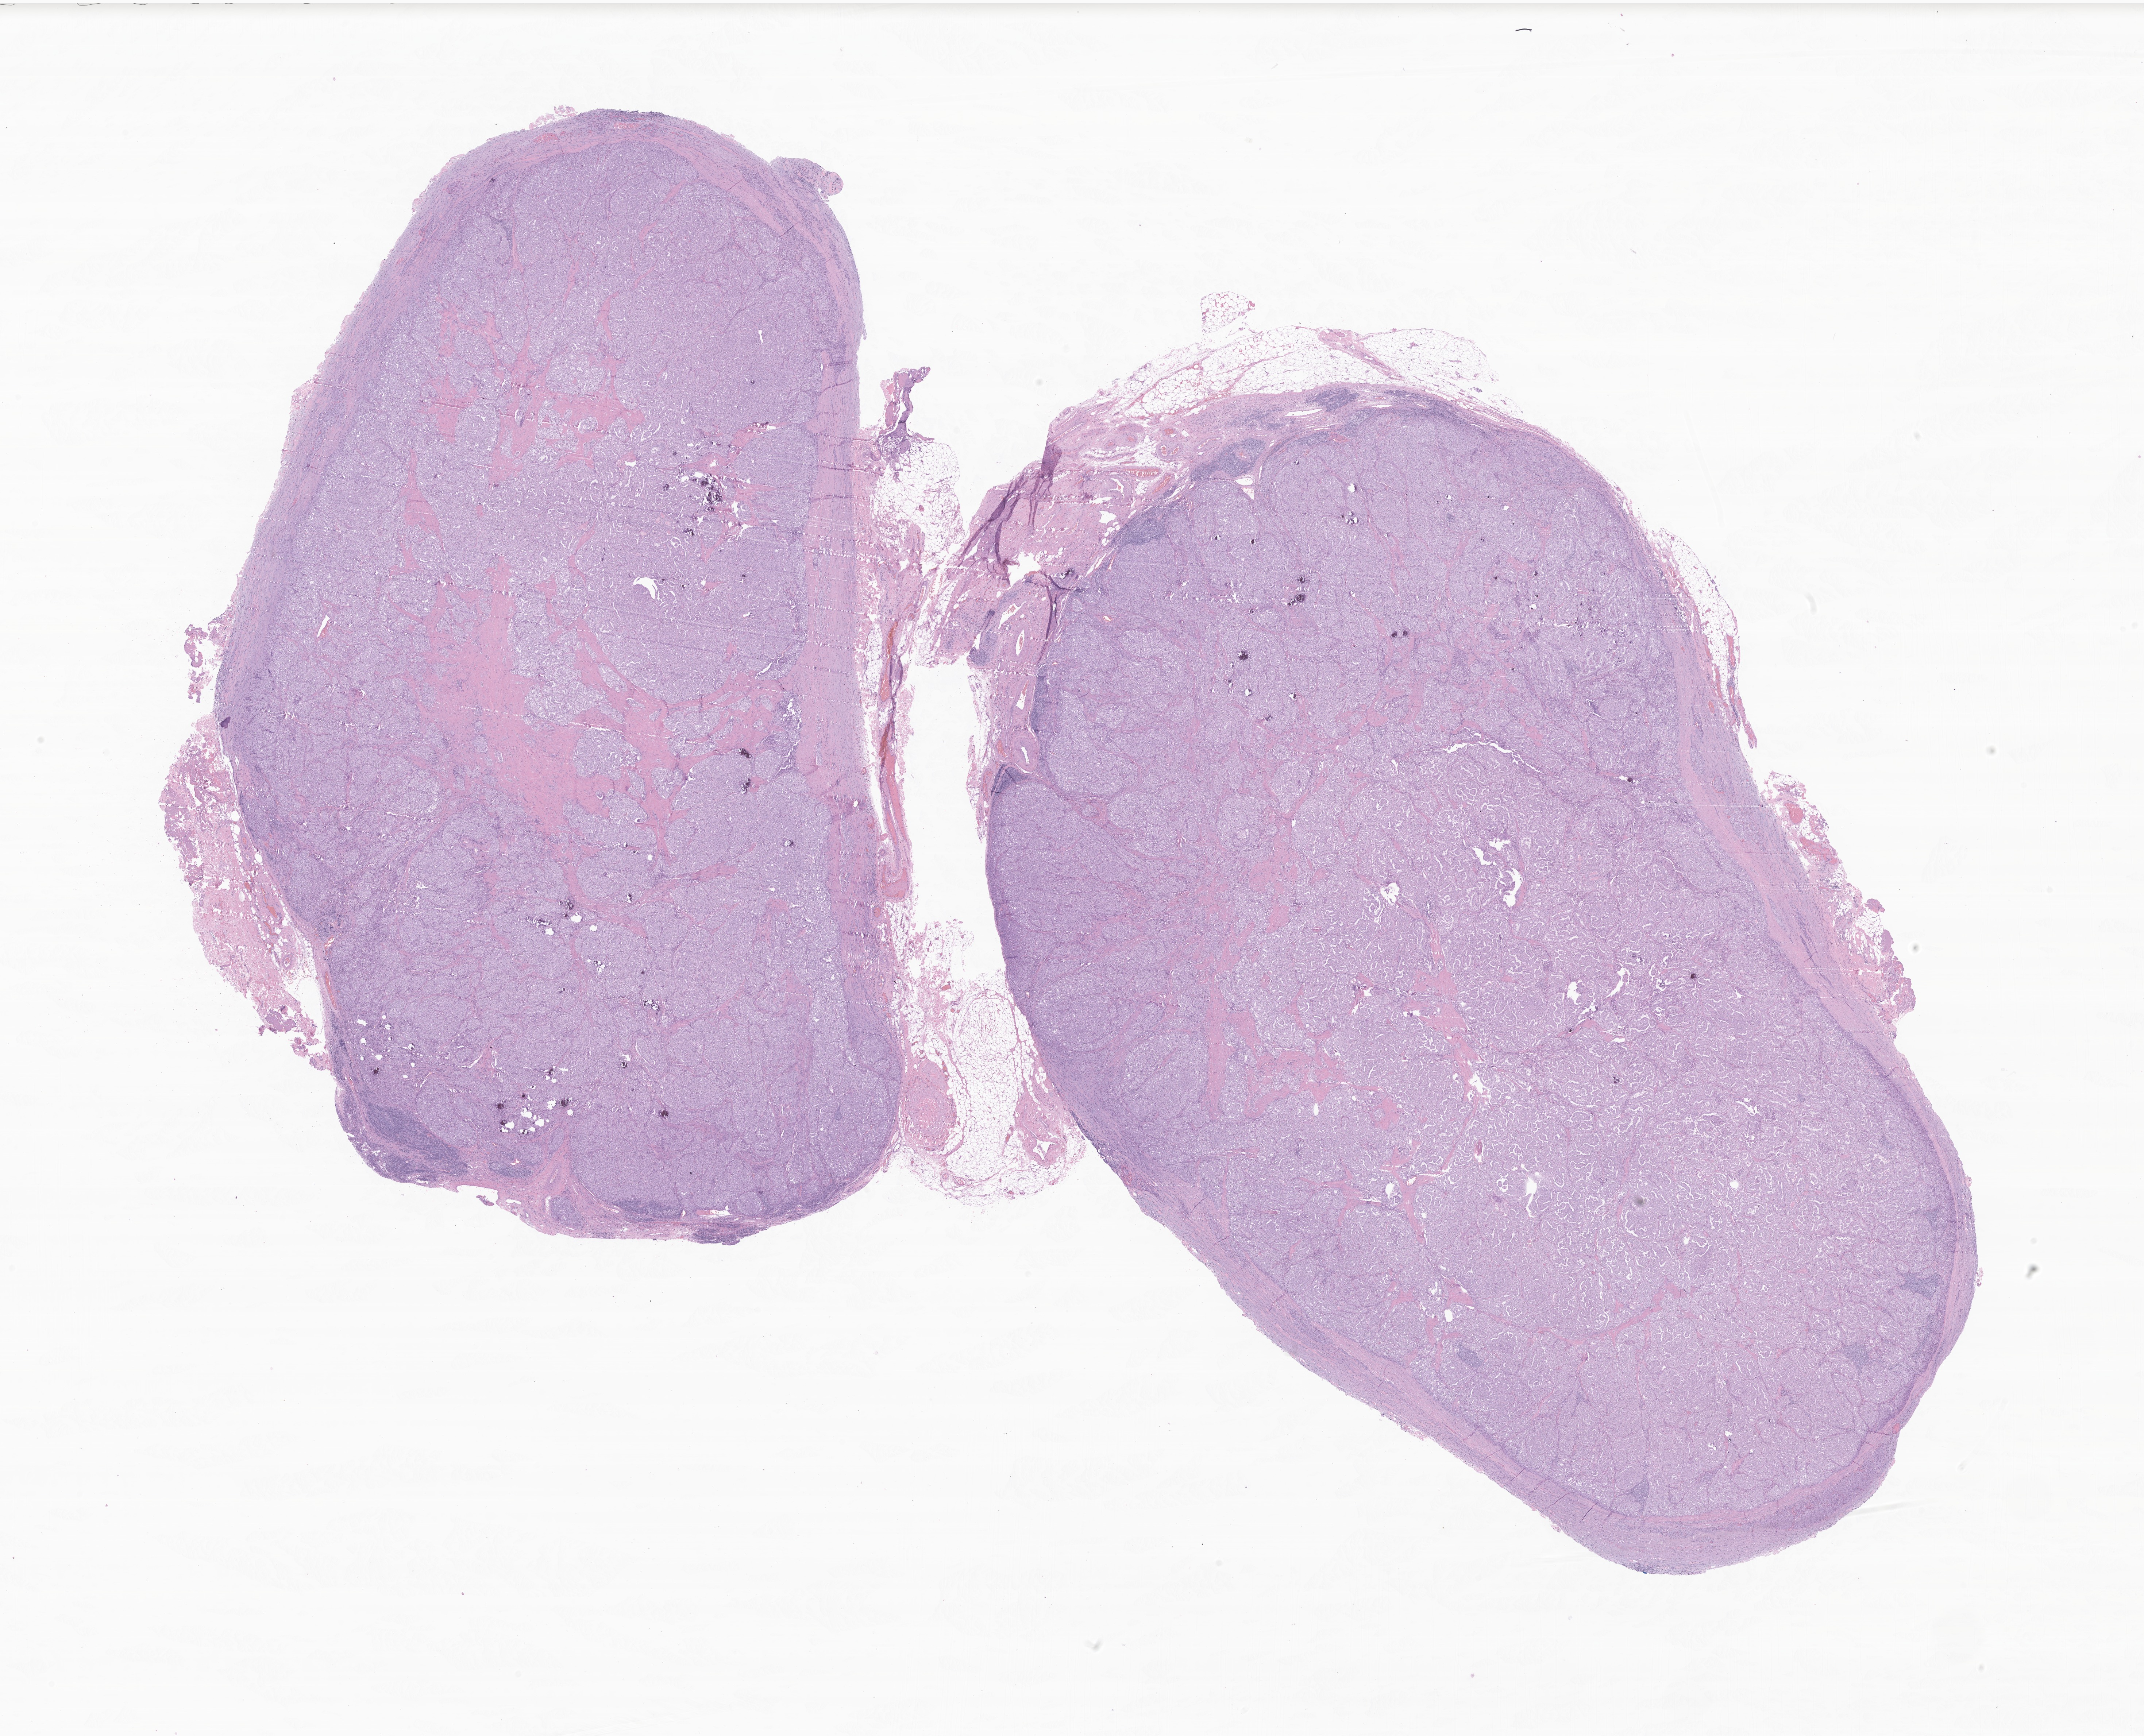
Whole-slide image, haematoxylin and eosin stain of tumor tissue from the thyroid — a low-resolution overview of the entire scanned area, about 24.8 x 20.1 mm, FFPE section. Patient: male, age 199 months (16 years 7 months).
Diagnosis (ICD-O-3 morphology term): Papillary carcinoma, NOS.